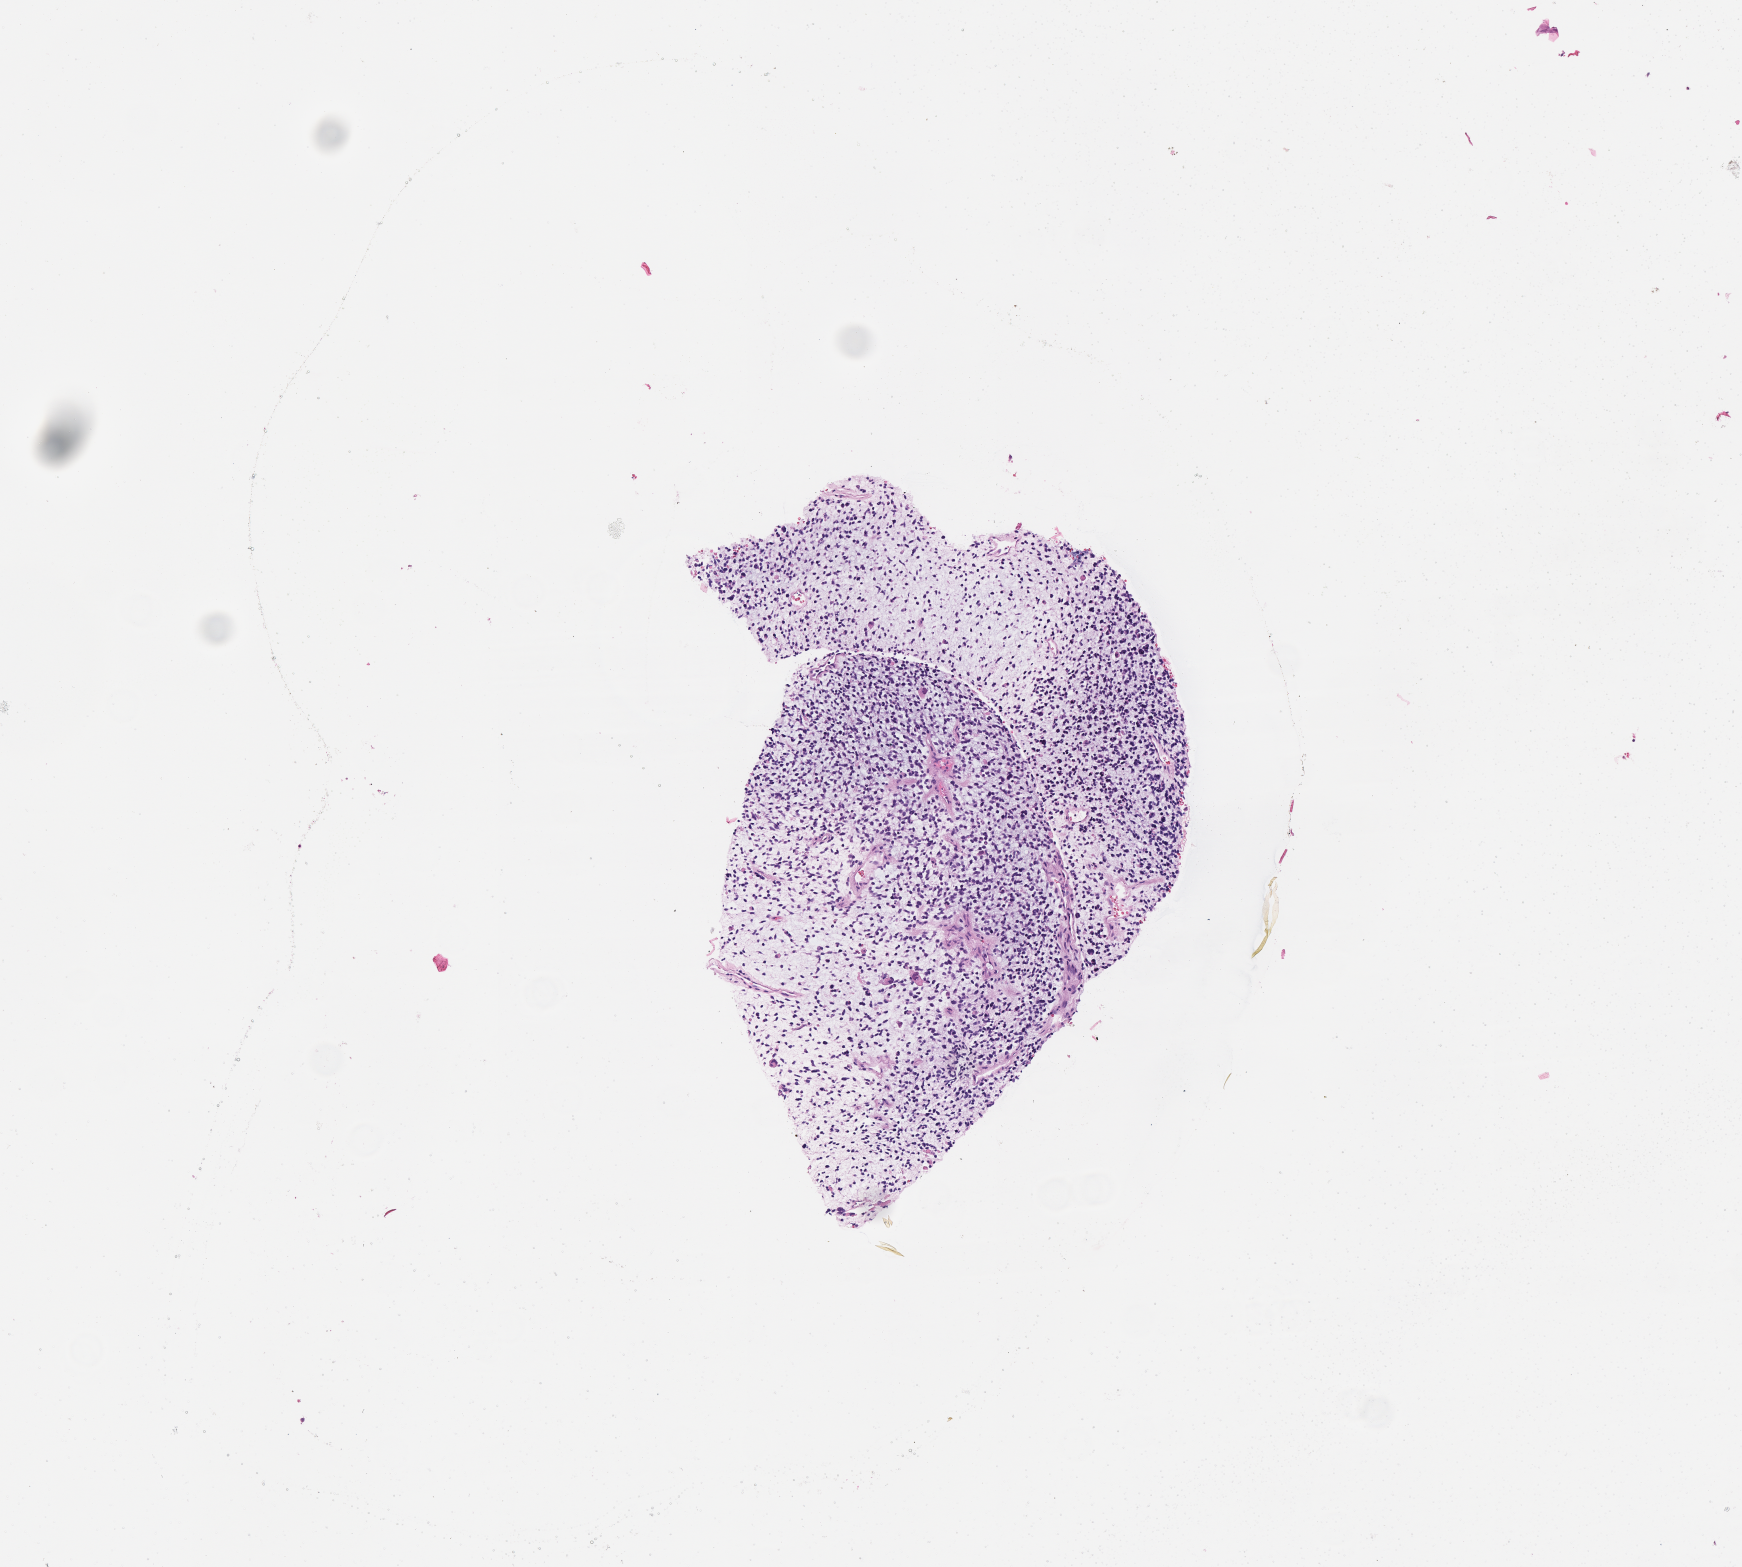
Digitized H&E-stained section of tumor tissue, a low-resolution overview of the entire scanned area, about 3.5 x 3.2 mm; FFPE section; sample anatomic site: prostate. Male patient, age at diagnosis 14.3 years.
Diagnosis: rhabdomyosarcoma; histological classification: embryonal rhabdomyosarcoma. Metastatic status at presentation (as recorded): metastatic (confirmed). Stage (as recorded): 4.